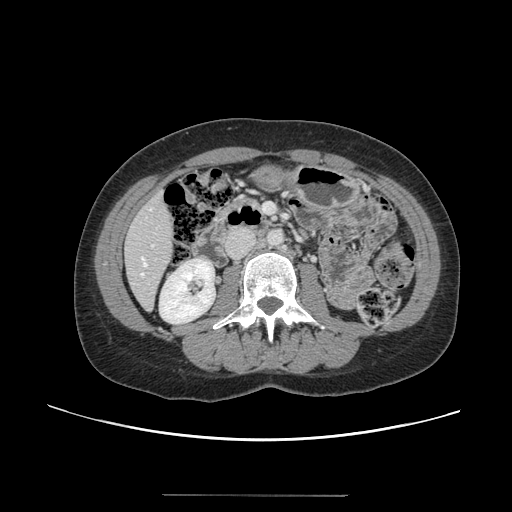
Contrast-enhanced abdominal CT, one axial slice; 120 kVp; soft-tissue window (W 400 / L 40 HU); 2.5 mm slice thickness; 512 × 512 image matrix. Female patient, age 53 years. From the clinical record (not read from this slice): diagnosis: colorectal cancer liver metastases, imaged before liver resection; multiple liver metastases: yes; largest metastasis: 1.1 cm; disease in both lobes: no.
Outlined on this slice (outlined manually by an expert reader):
- hepatic veins: bounding box (x1, y1, x2, y2) in pixels: (142, 258, 147, 276)
- liver: (125, 194, 174, 309)
- planned liver remnant (the part of the liver to remain after resection): (126, 194, 174, 308)
- portal vein (with intrahepatic branches): (151, 245, 155, 247)